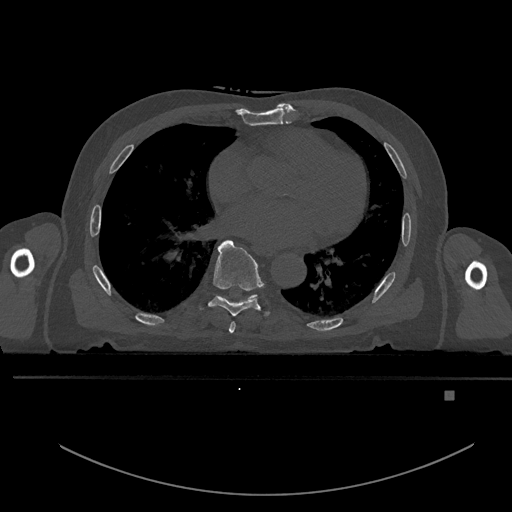
CT including the spine, one axial slice. Slice 250 of 969 in the series (ordered by position). Bone window (W 1800 / L 400 HU). 0.5 mm slice thickness. 512 × 512 image matrix, field of view 456 × 456 mm. Patient: male, 82 years. From the clinical record (not read from this slice): primary cancer: prostate; vertebrae with lytic lesions (as recorded): T11, T9, T8, T2.
Annotated regions visible in this slice (semi-automatic segmentation, software-assisted and operator-edited):
- T6 vertebra: bounding box [x1, y1, x2, y2] px = [229, 322, 236, 334]
- T7 vertebra: [200, 240, 271, 318]
- T8 vertebra: [217, 295, 258, 303]